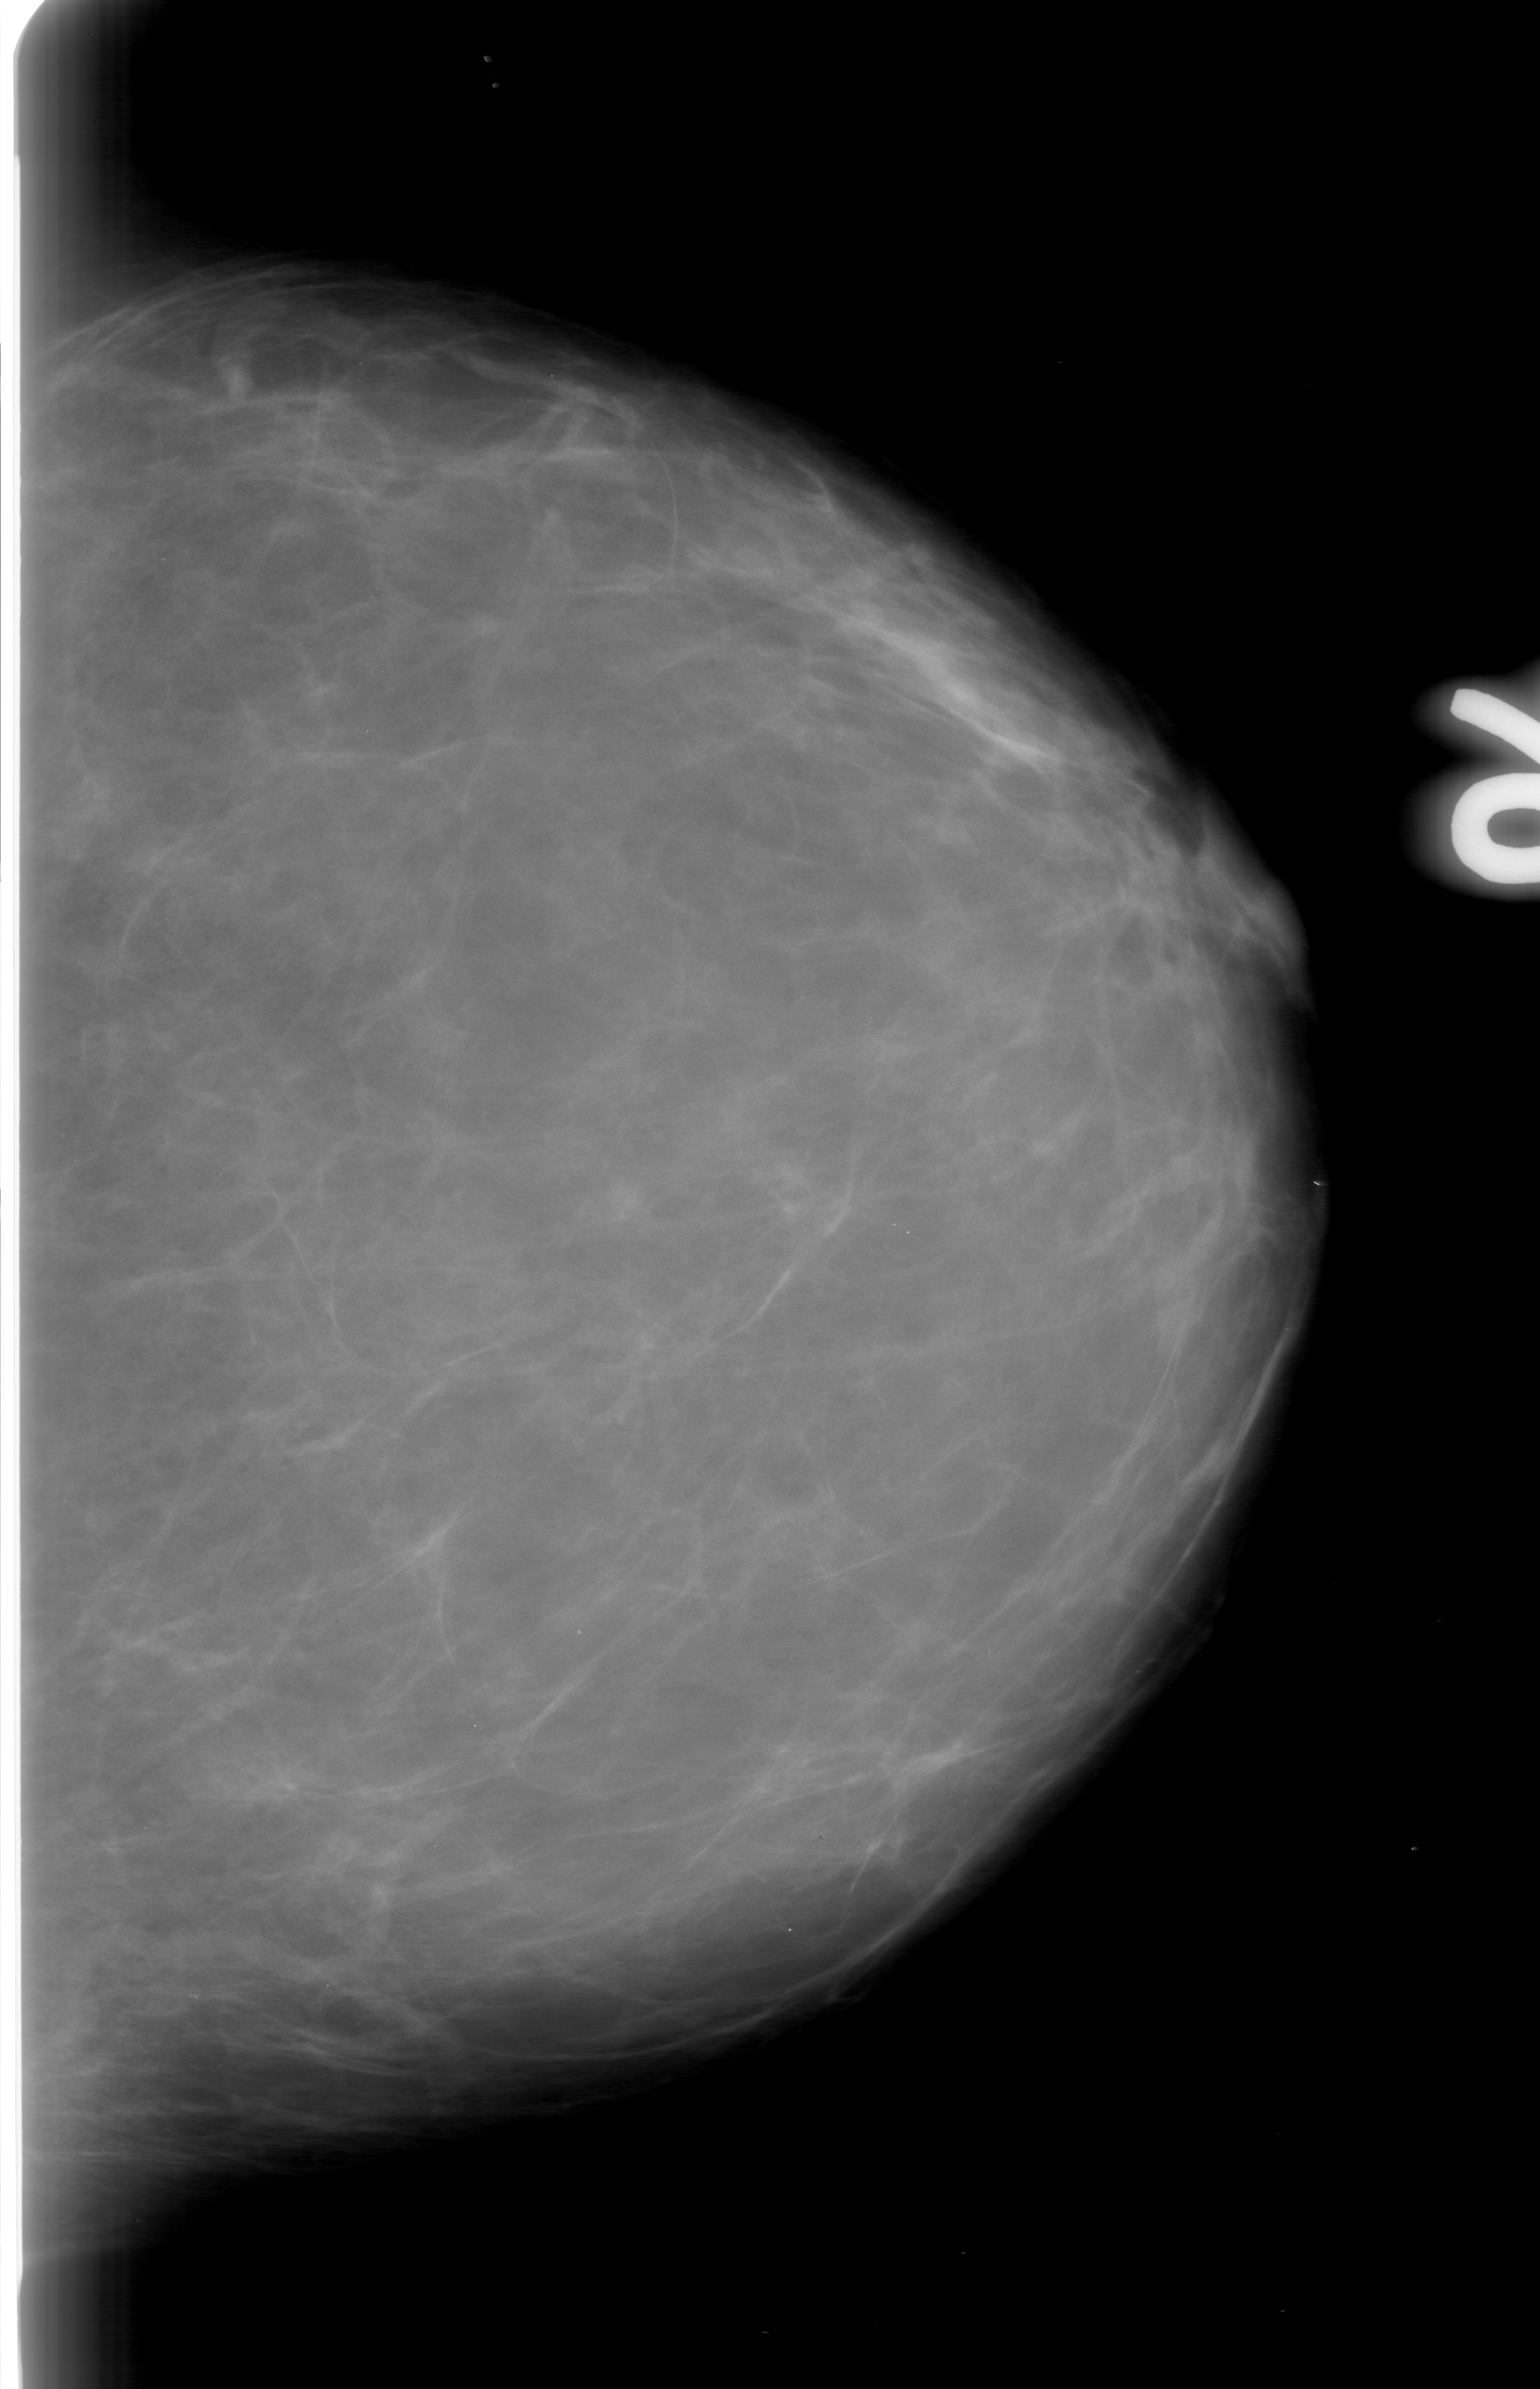
Mammogram (digitized film). Left breast. Craniocaudal (CC) view. Breast composition: almost entirely fatty (BI-RADS density category 1 of 4). 1540 × 2389 image matrix.
Expert-marked regions of interest on this film, with their recorded descriptors:
- mass, shape irregular, margins obscured; BI-RADS assessment category 0 (incomplete: needs additional imaging); subtlety rating 4 on a 1 (subtle) to 5 (obvious) scale; pathology result (as recorded, not read from the image): benign: box from (x=15, y=711) to (x=146, y=862) px